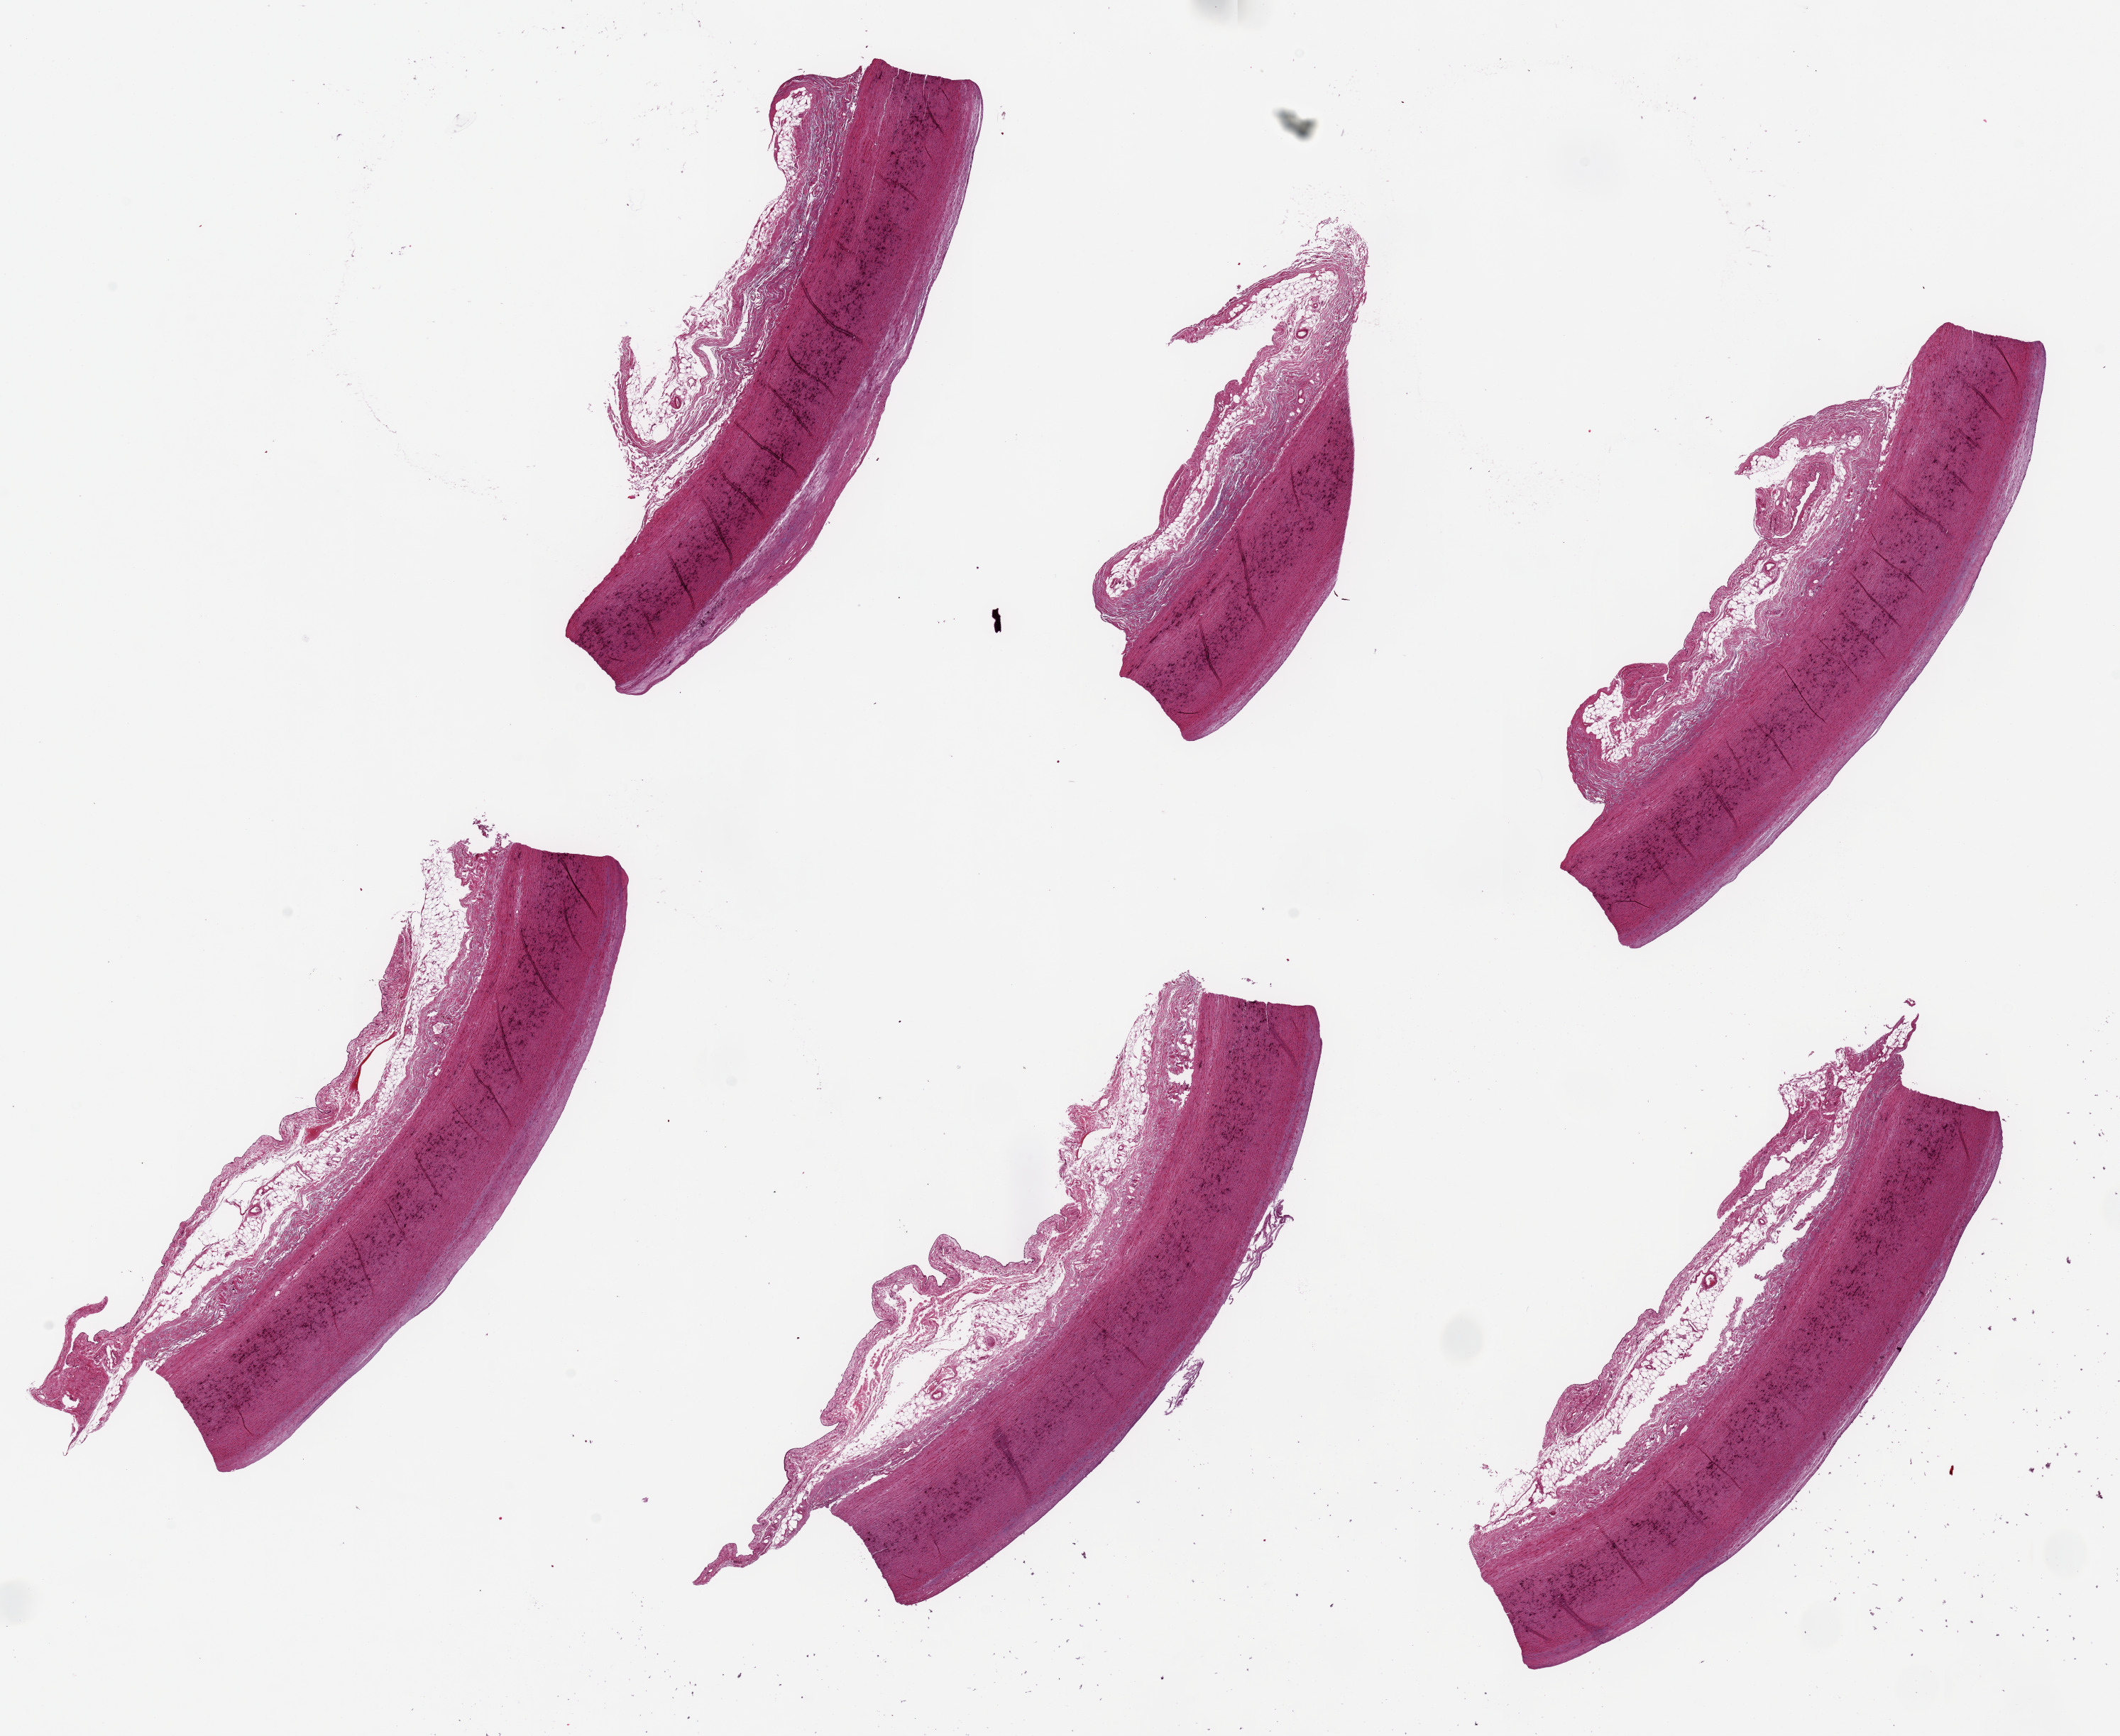
Digitized hematoxylin and eosin (H&E)-stained section — low-resolution overview of the scanned area, about 23.6 x 19.3 mm (from a 20x scan). PAXgene-fixed paraffin-embedded (PFPE) section. Target tissue: aorta. Tissue donor sample. Donor sex: male.
Reviewer comment on this tissue sample: 6 pieces ~7x1.5mm, up to ~0.5mm atherosis on luminal surface, up to~1mm adherent fibroadipose tissue on adventia.